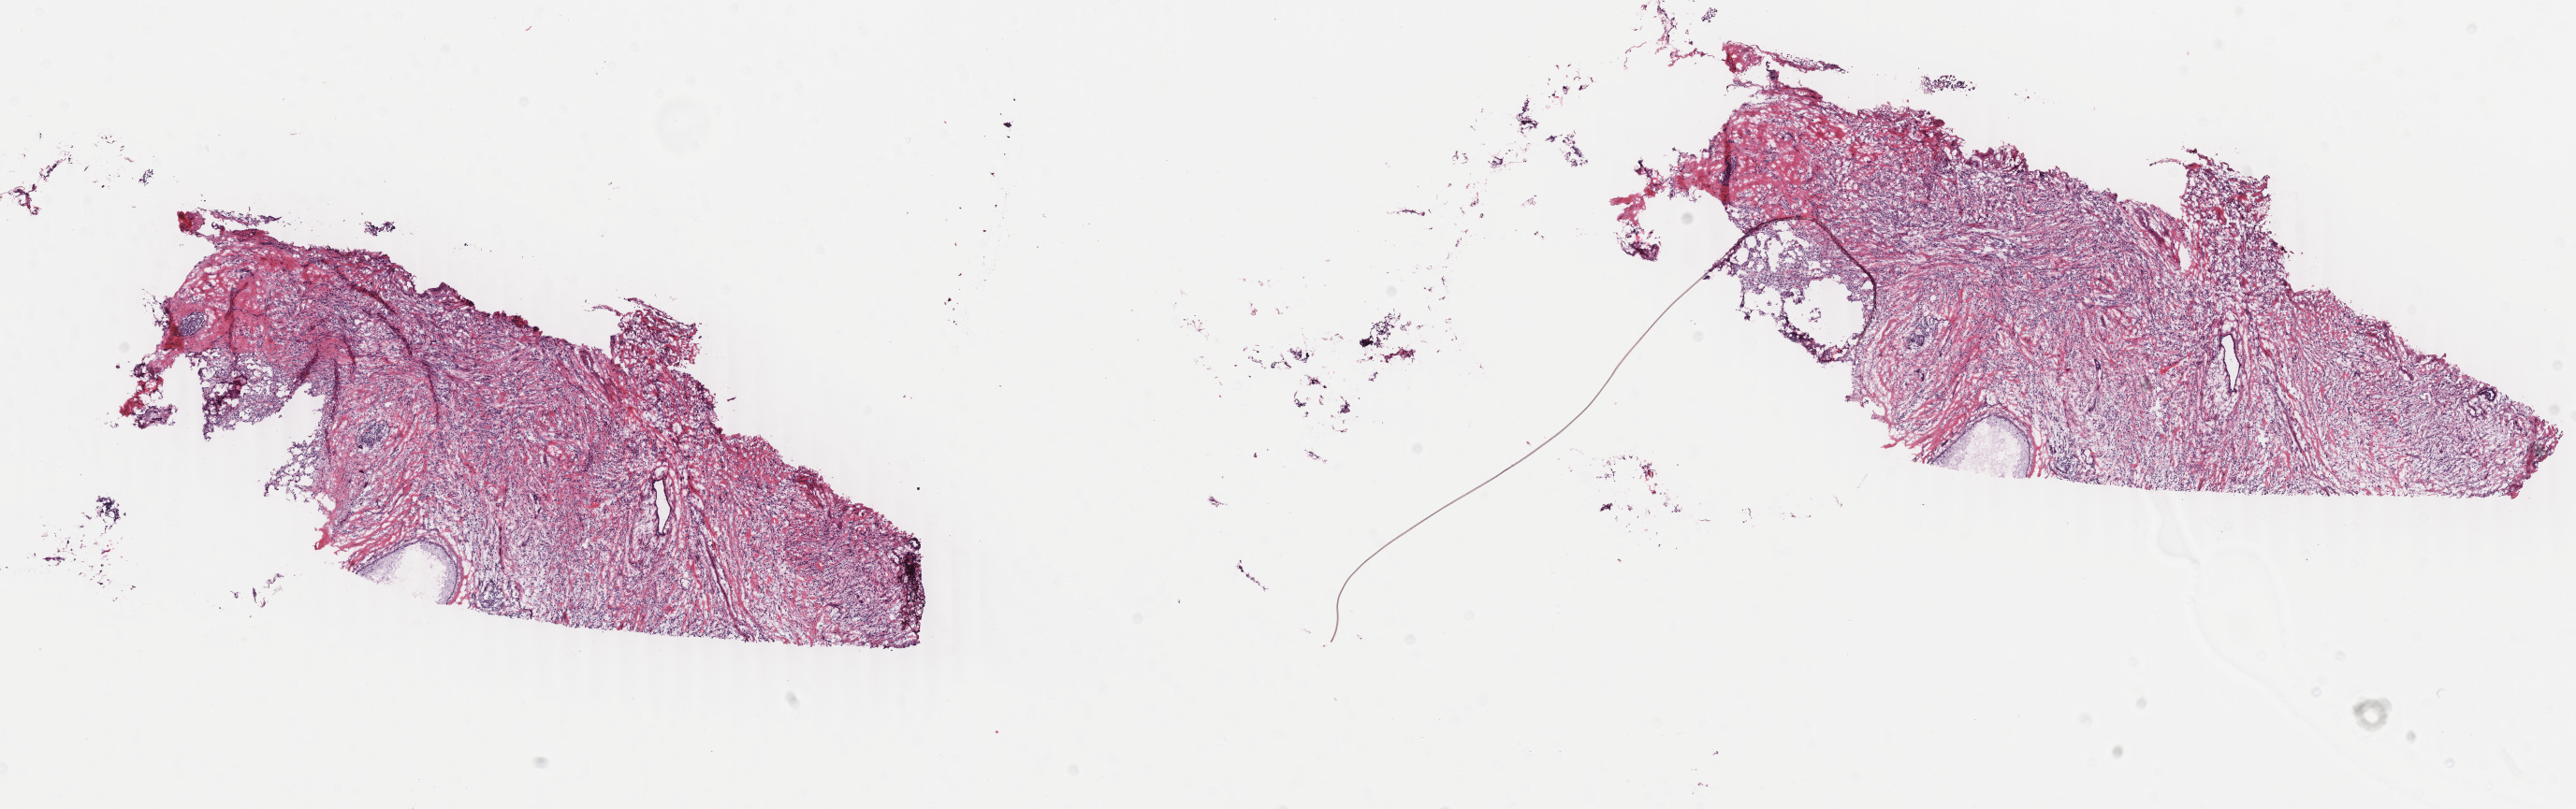
Whole-slide histology image, H&E-stained, a low-resolution overview of the entire scanned area, about 21.9 x 6.9 mm (from a 40x scan); frozen section from the top of the tissue portion; sample: primary tumour, breast. Female patient; age at initial diagnosis 63 years. Slide review estimates, as recorded: tumour cells 85%, tumour nuclei 85%.
Diagnosis: Lobular carcinoma, NOS.